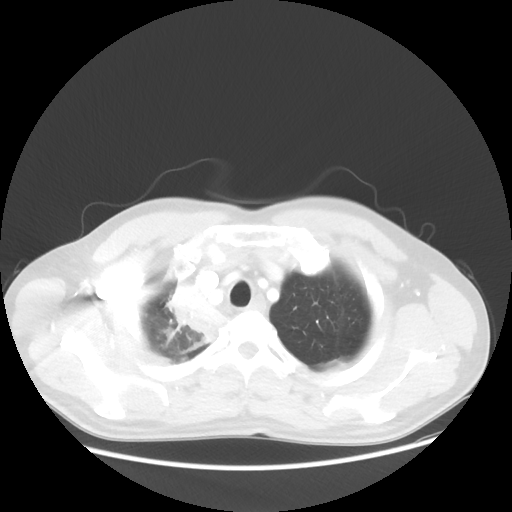
Chest CT, one axial slice; slice 47 of 56 in the series (ordered by position); reconstruction kernel STANDARD; 100 kVp; lung window (W 1500 / L -600 HU); 512 × 512 image matrix, field of view 398 × 398 mm. Patient: male, 60 years. From the clinical record (not read from this slice): clinical TNM (as recorded): T2a N1 M0.
Annotated regions visible in this slice (rectangle marked by the reading radiologist):
- lung tumour (recorded histology: squamous cell carcinoma): bounding box (x1, y1, x2, y2) in pixels: (161, 272, 225, 365)